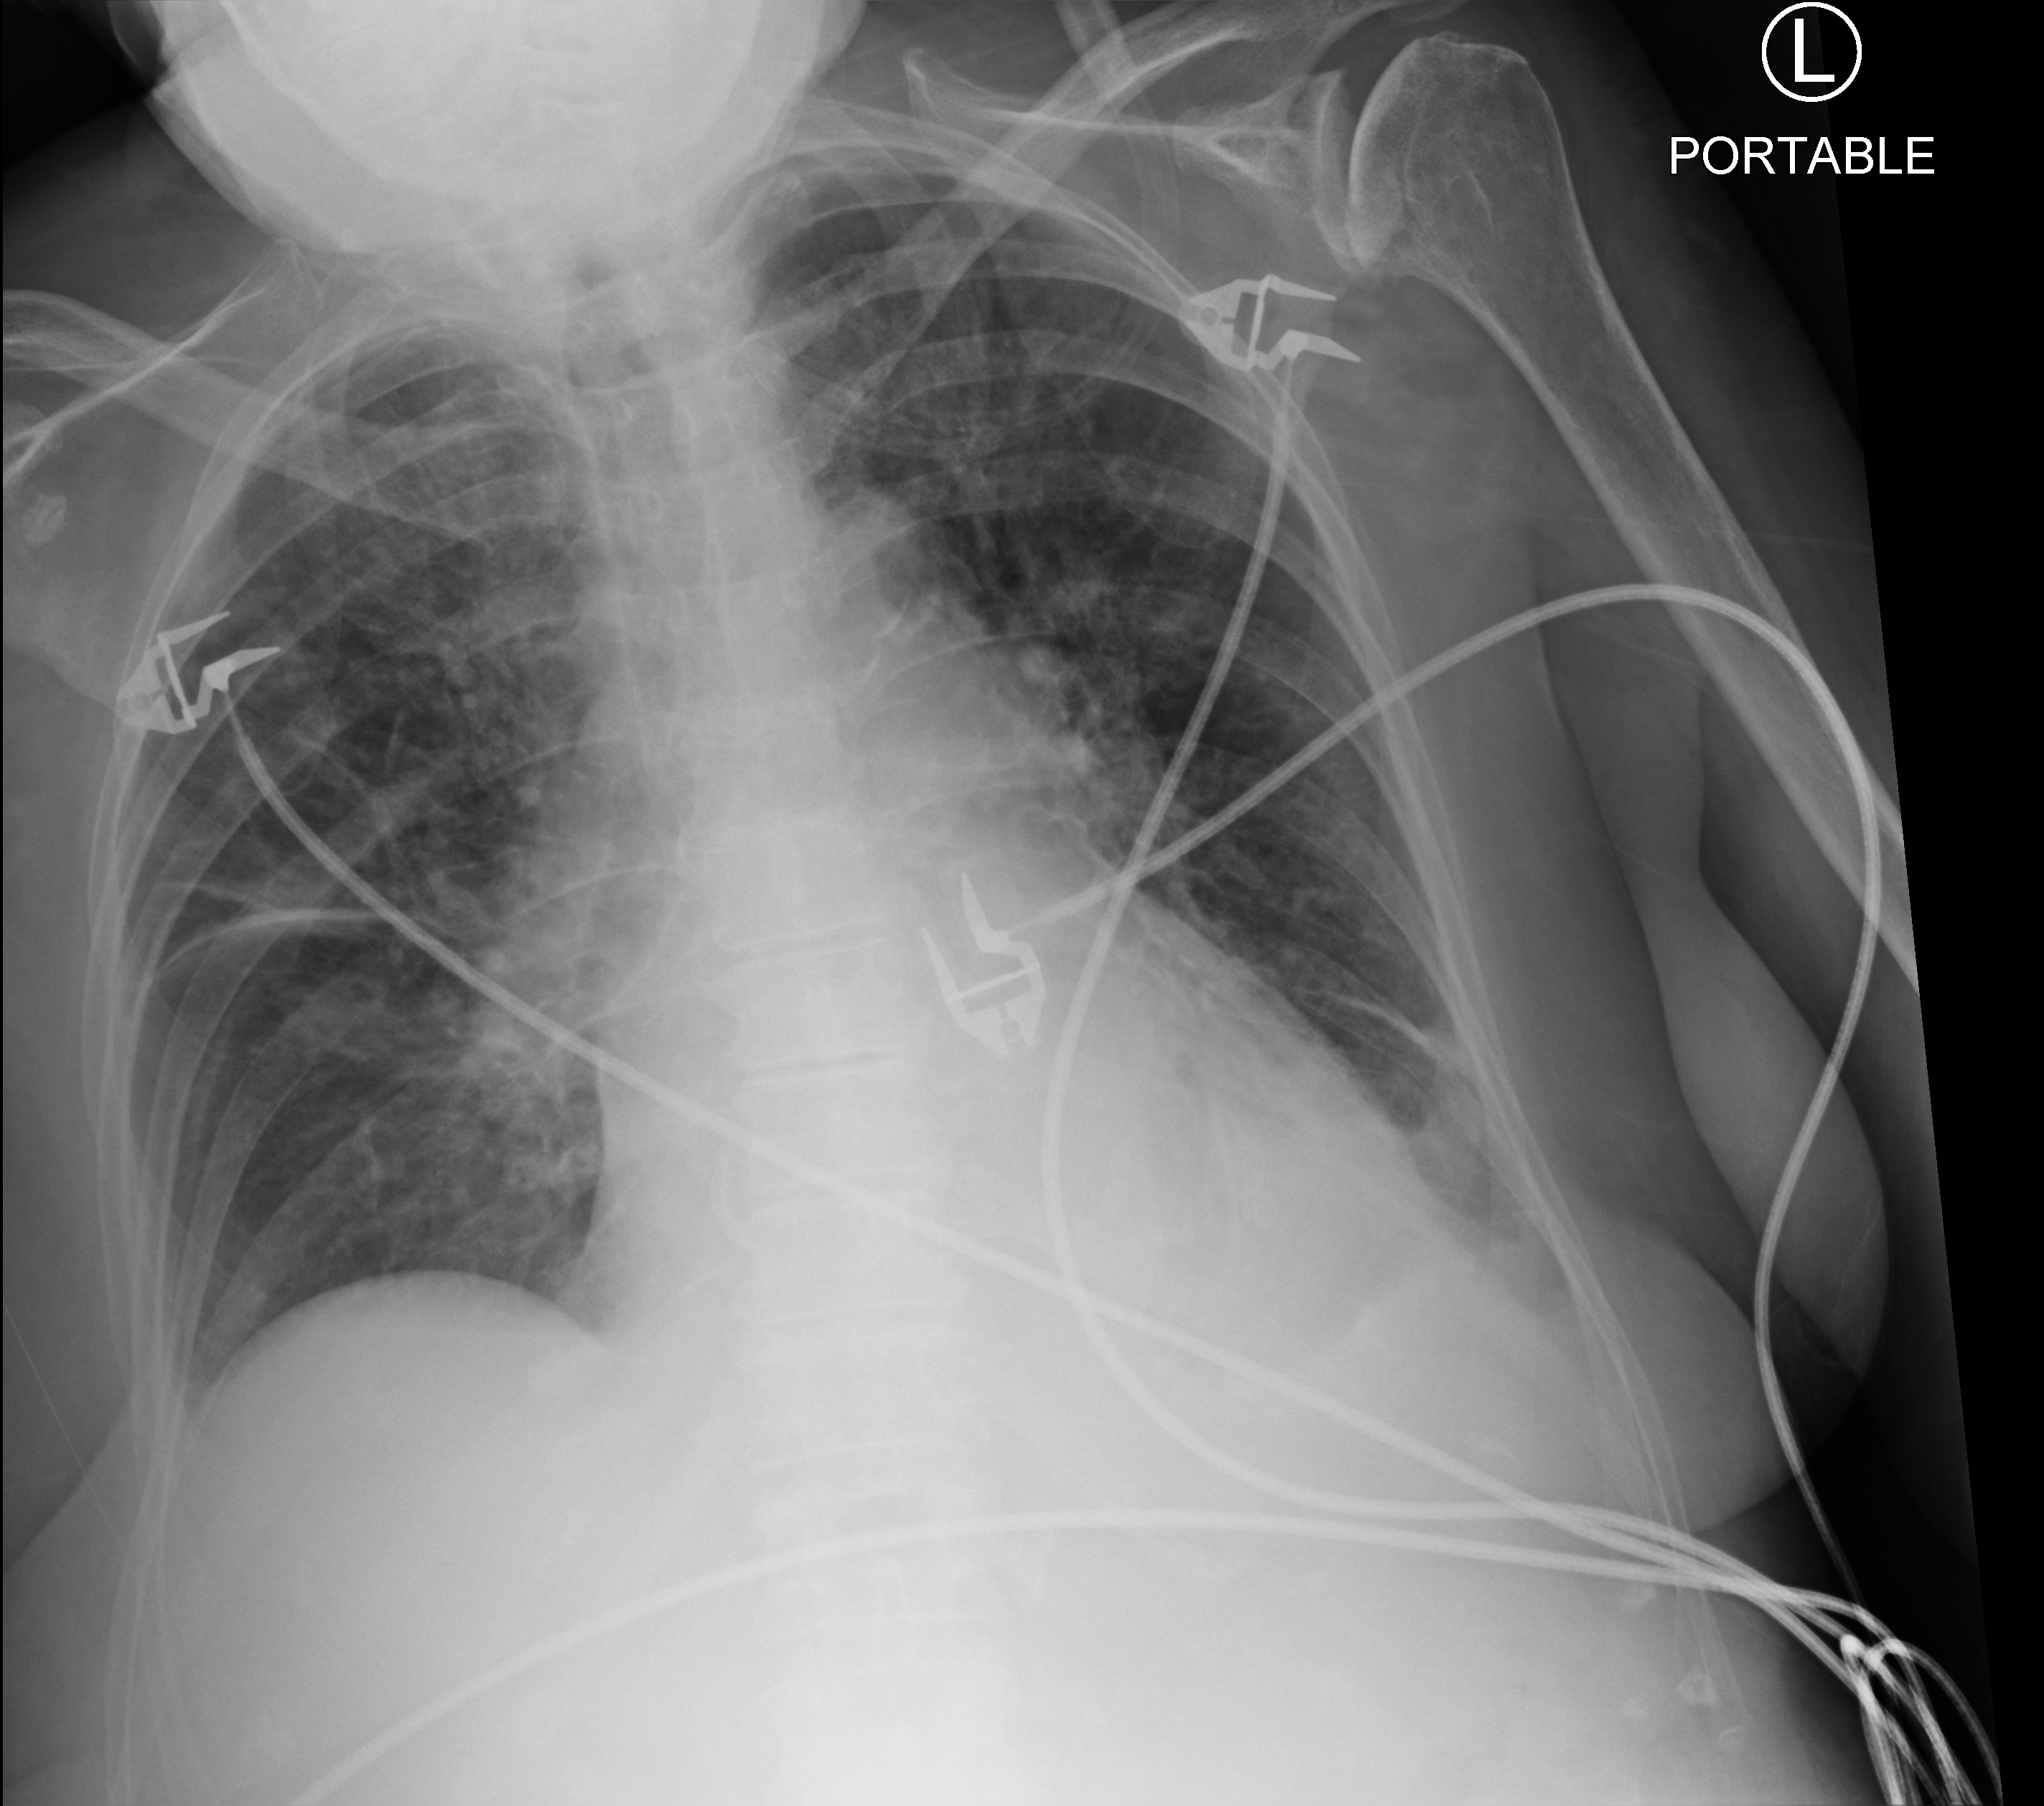
Chest X-ray (portable). Patient hospitalised with COVID-19; female, aged 75–90 years.
Hospital-stay facts (about this admission, not read from this image; timing relative to this image not recorded): admitted to intensive care during this hospital stay: no.